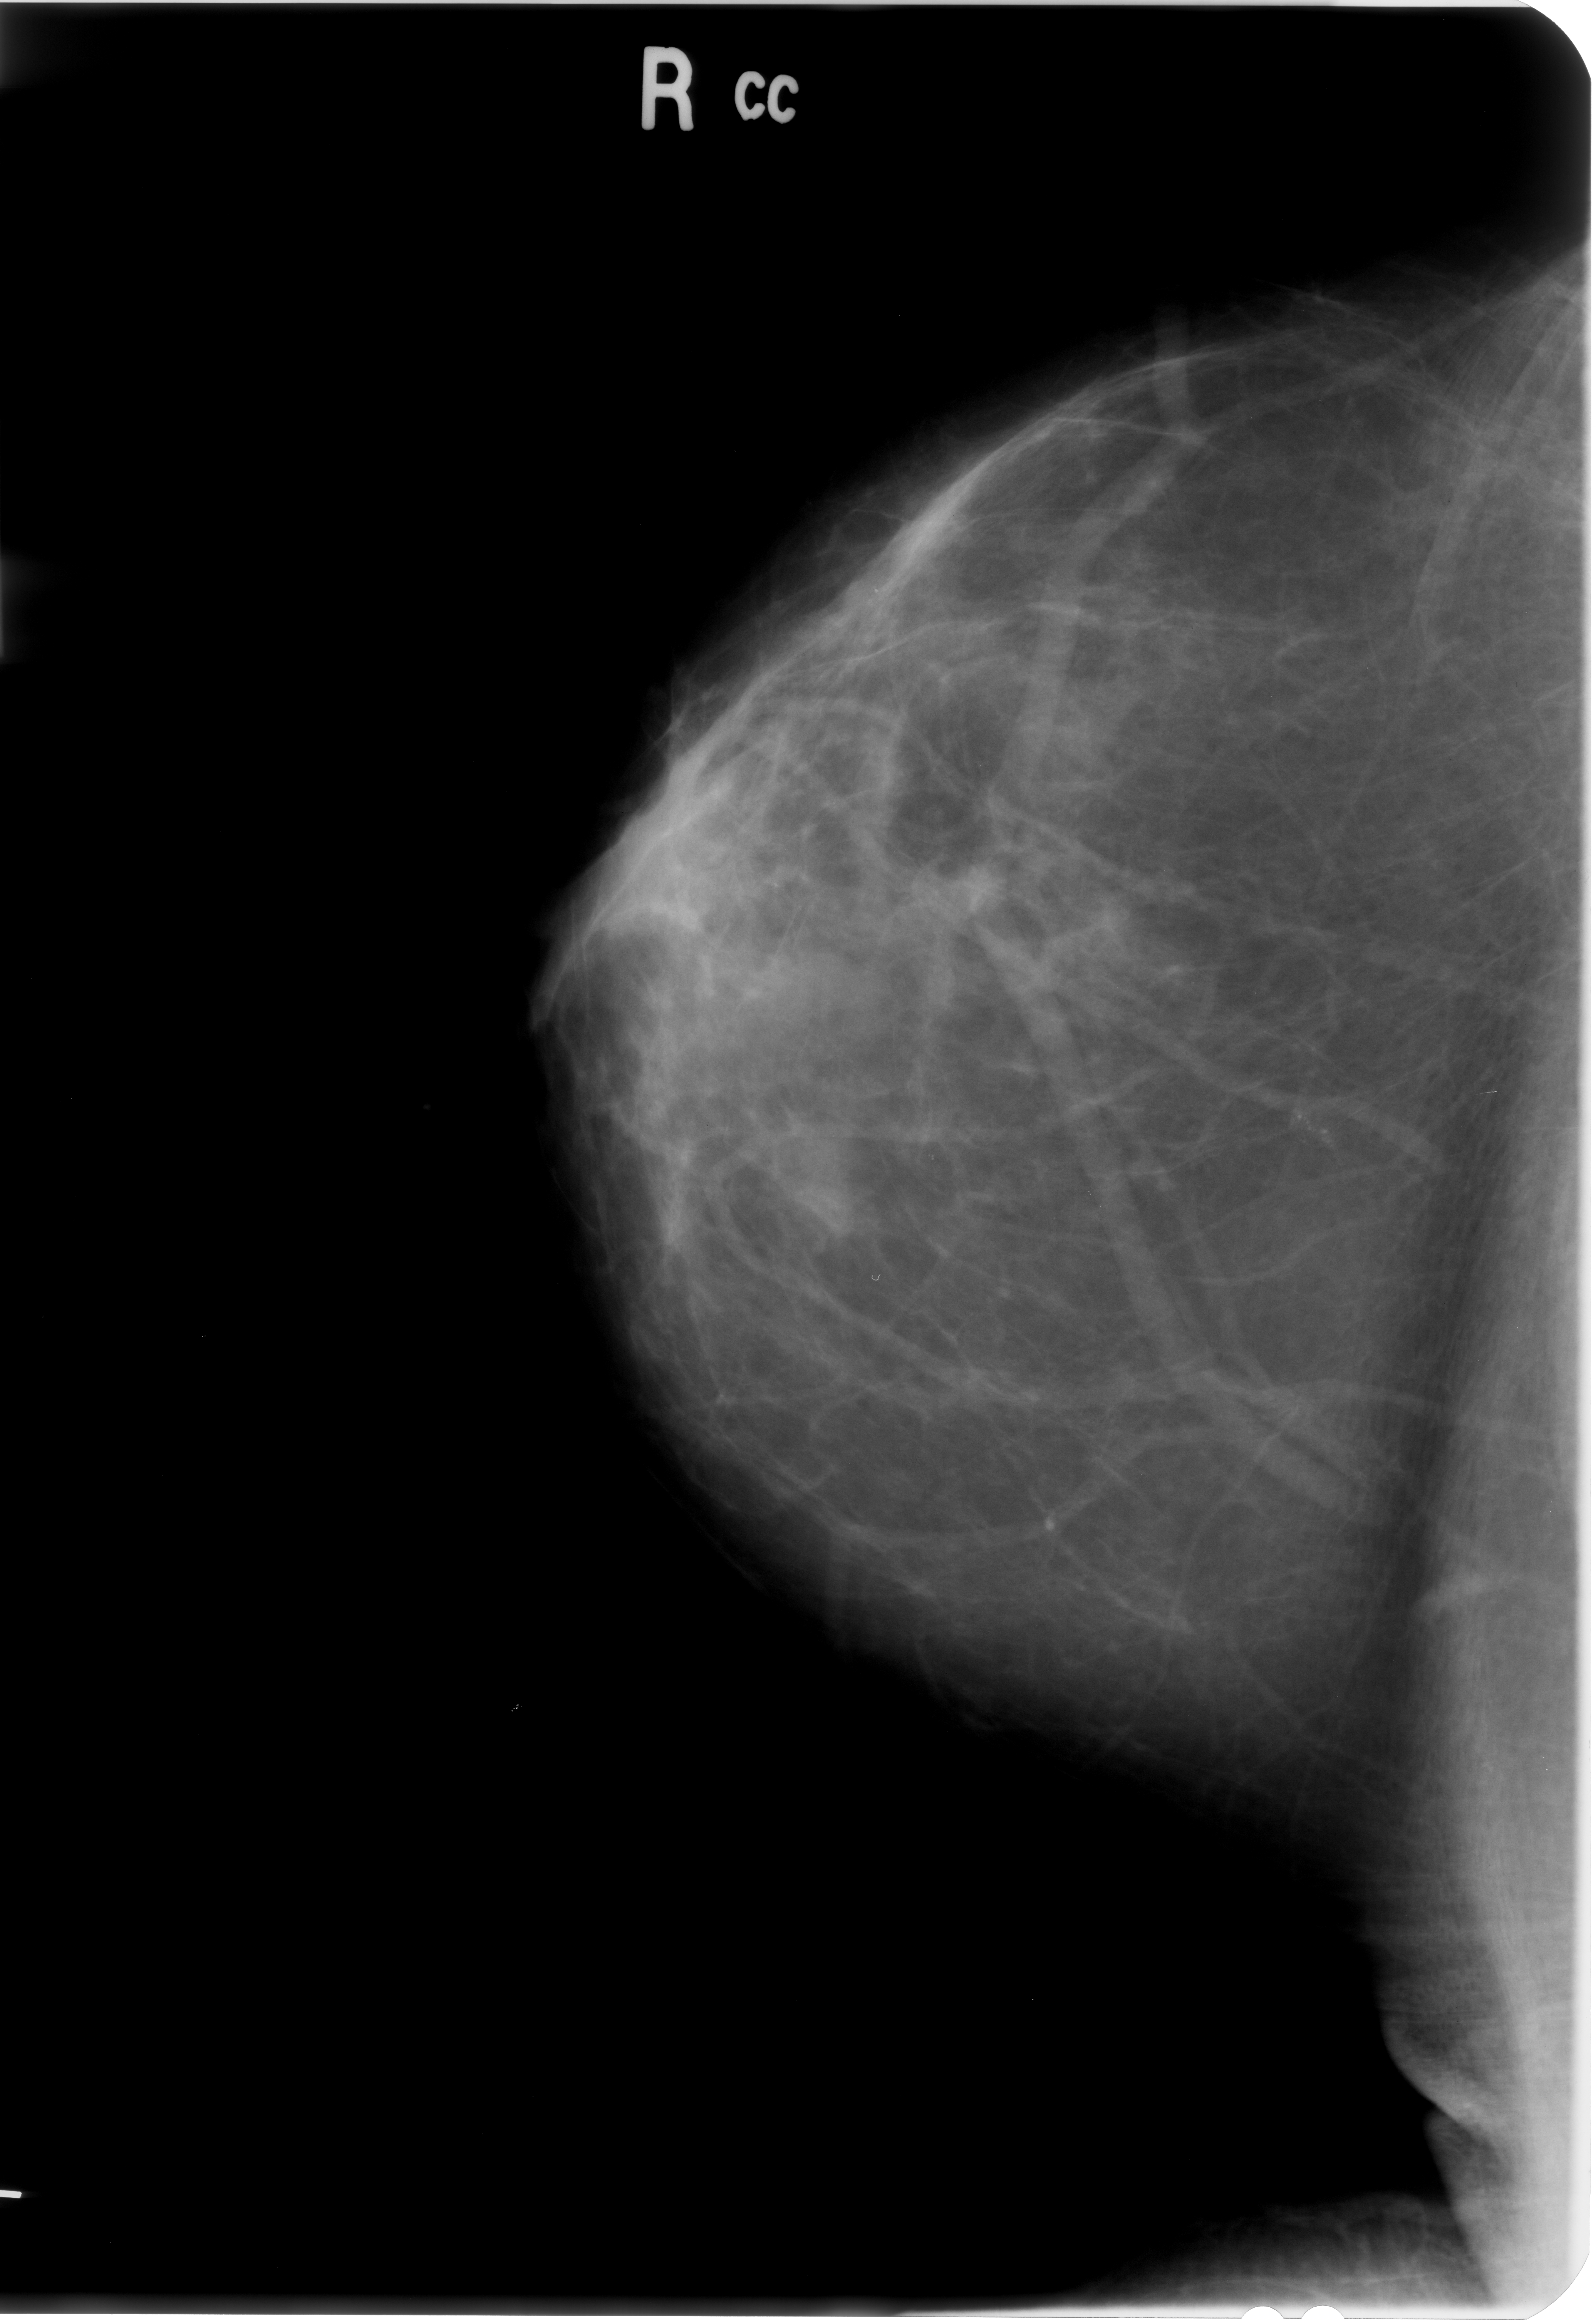
Scanned film-screen mammogram, right breast, craniocaudal (CC) view, breast composition: almost entirely fatty (BI-RADS density category 1 of 4).
Radiologist-marked abnormalities on this image: calcifications, morphology pleomorphic, distribution clustered; BI-RADS assessment category 4; subtlety rating 3 on a 1 (subtle) to 5 (obvious) scale; pathology (as recorded): benign.